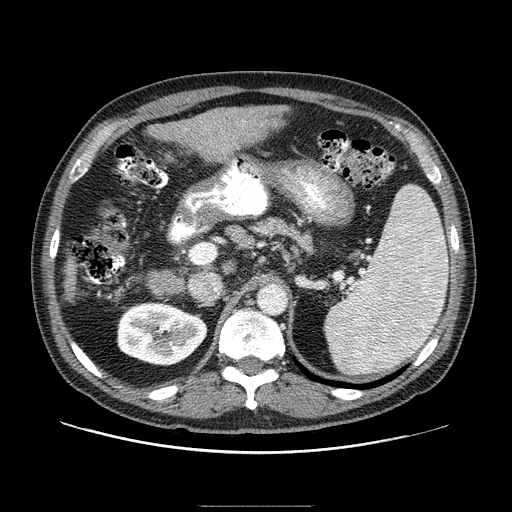
Contrast-enhanced abdominal CT (liver protocol), one axial slice. Position 45 of 99 along the scan axis. Reconstruction kernel STANDARD. 100 kVp. One of 2 acquisitions stored at this slice position. Soft-tissue window (W 400 / L 40 HU). 512 × 512 image matrix, field of view 400 × 400 mm. Case-level facts recorded for this patient, not image findings: diagnosis: hepatocellular carcinoma (patient treated with transarterial chemoembolisation; whether this scan precedes or follows treatment is not stated here); TNM stage (as recorded): Stage-II; Child-Pugh class: A; tumour differentiation: well differentiated.
Structures marked on this image (semi-automatically segmented with operator editing):
- liver parenchyma outside the tumour (the mass and vessels are separate outlines, so this box may not span the whole liver): box from (x=64, y=106) to (x=280, y=300) px